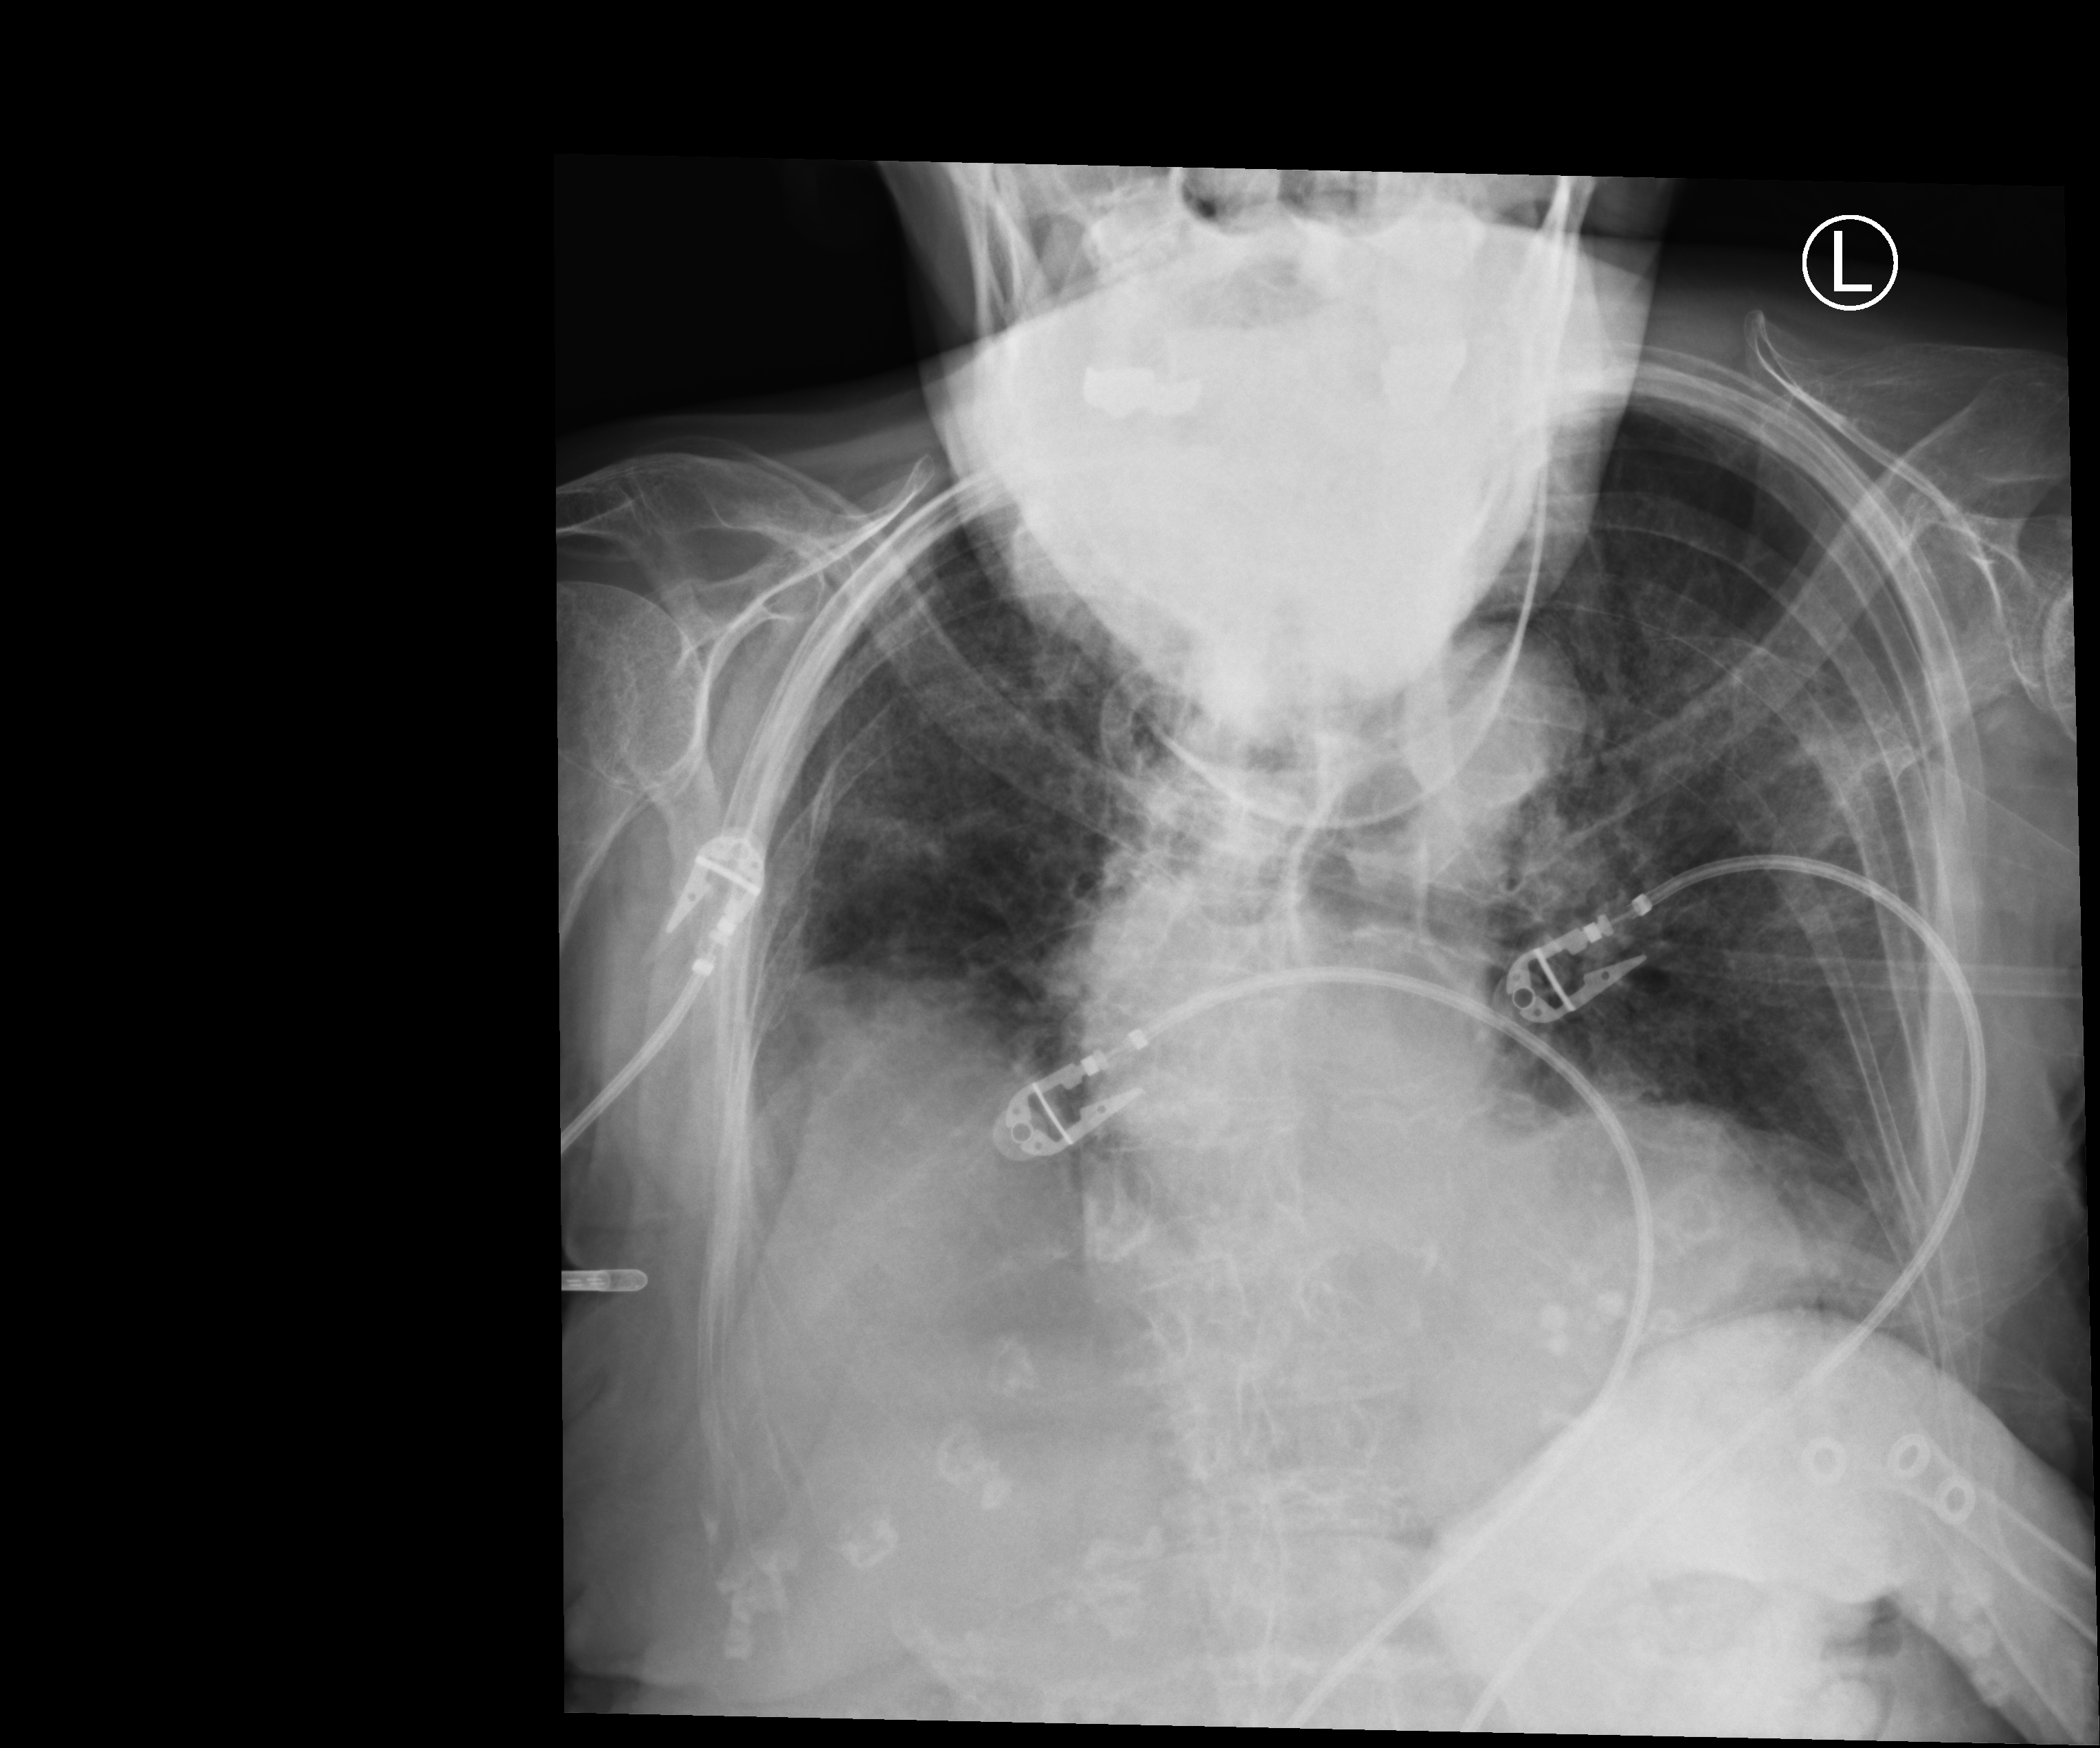
Chest X-ray (portable). Female patient hospitalised with COVID-19, age 75–90 years.
From the hospital-stay record, not from the radiograph (when in the stay this image was taken is not recorded): length of hospital stay: 6 days.